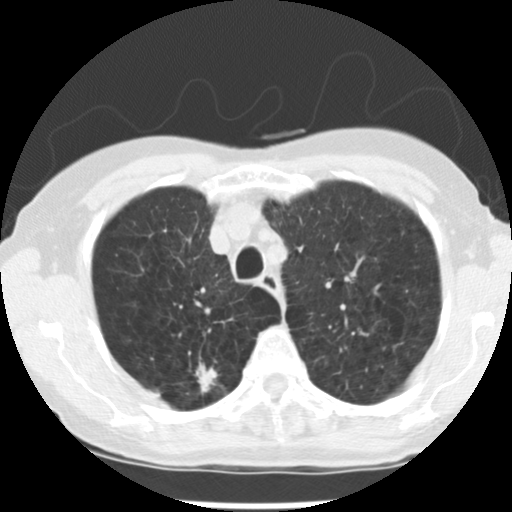
Chest CT (low-dose screening protocol), one axial image; baseline annual screen; lung window (W 1500 / L -600 HU); 2.5 mm slice thickness; slice 51 of 265 in the series. Female, age 72 years at enrolment. Current smoker at enrolment.
- Lesion marked by an expert reader, bounding box (x1, y1, x2, y2) in pixels: (183, 358, 235, 406).
- The screening reader recorded 3 non-calcified nodules or masses ≥4 mm on this exam; which of them this box marks is not recorded.
- Official screen result: positive, change unspecified: nodule(s) >= 4 mm or enlarging nodule(s), mass(es), or other non-specific abnormalities suspicious for lung cancer.
- Later outcome: lung cancer diagnosed 50 days after this screen — adenocarcinoma, NOS, right upper lobe, moderately differentiated (G2), stage IB (AJCC 6th edition), 22 mm at pathology.